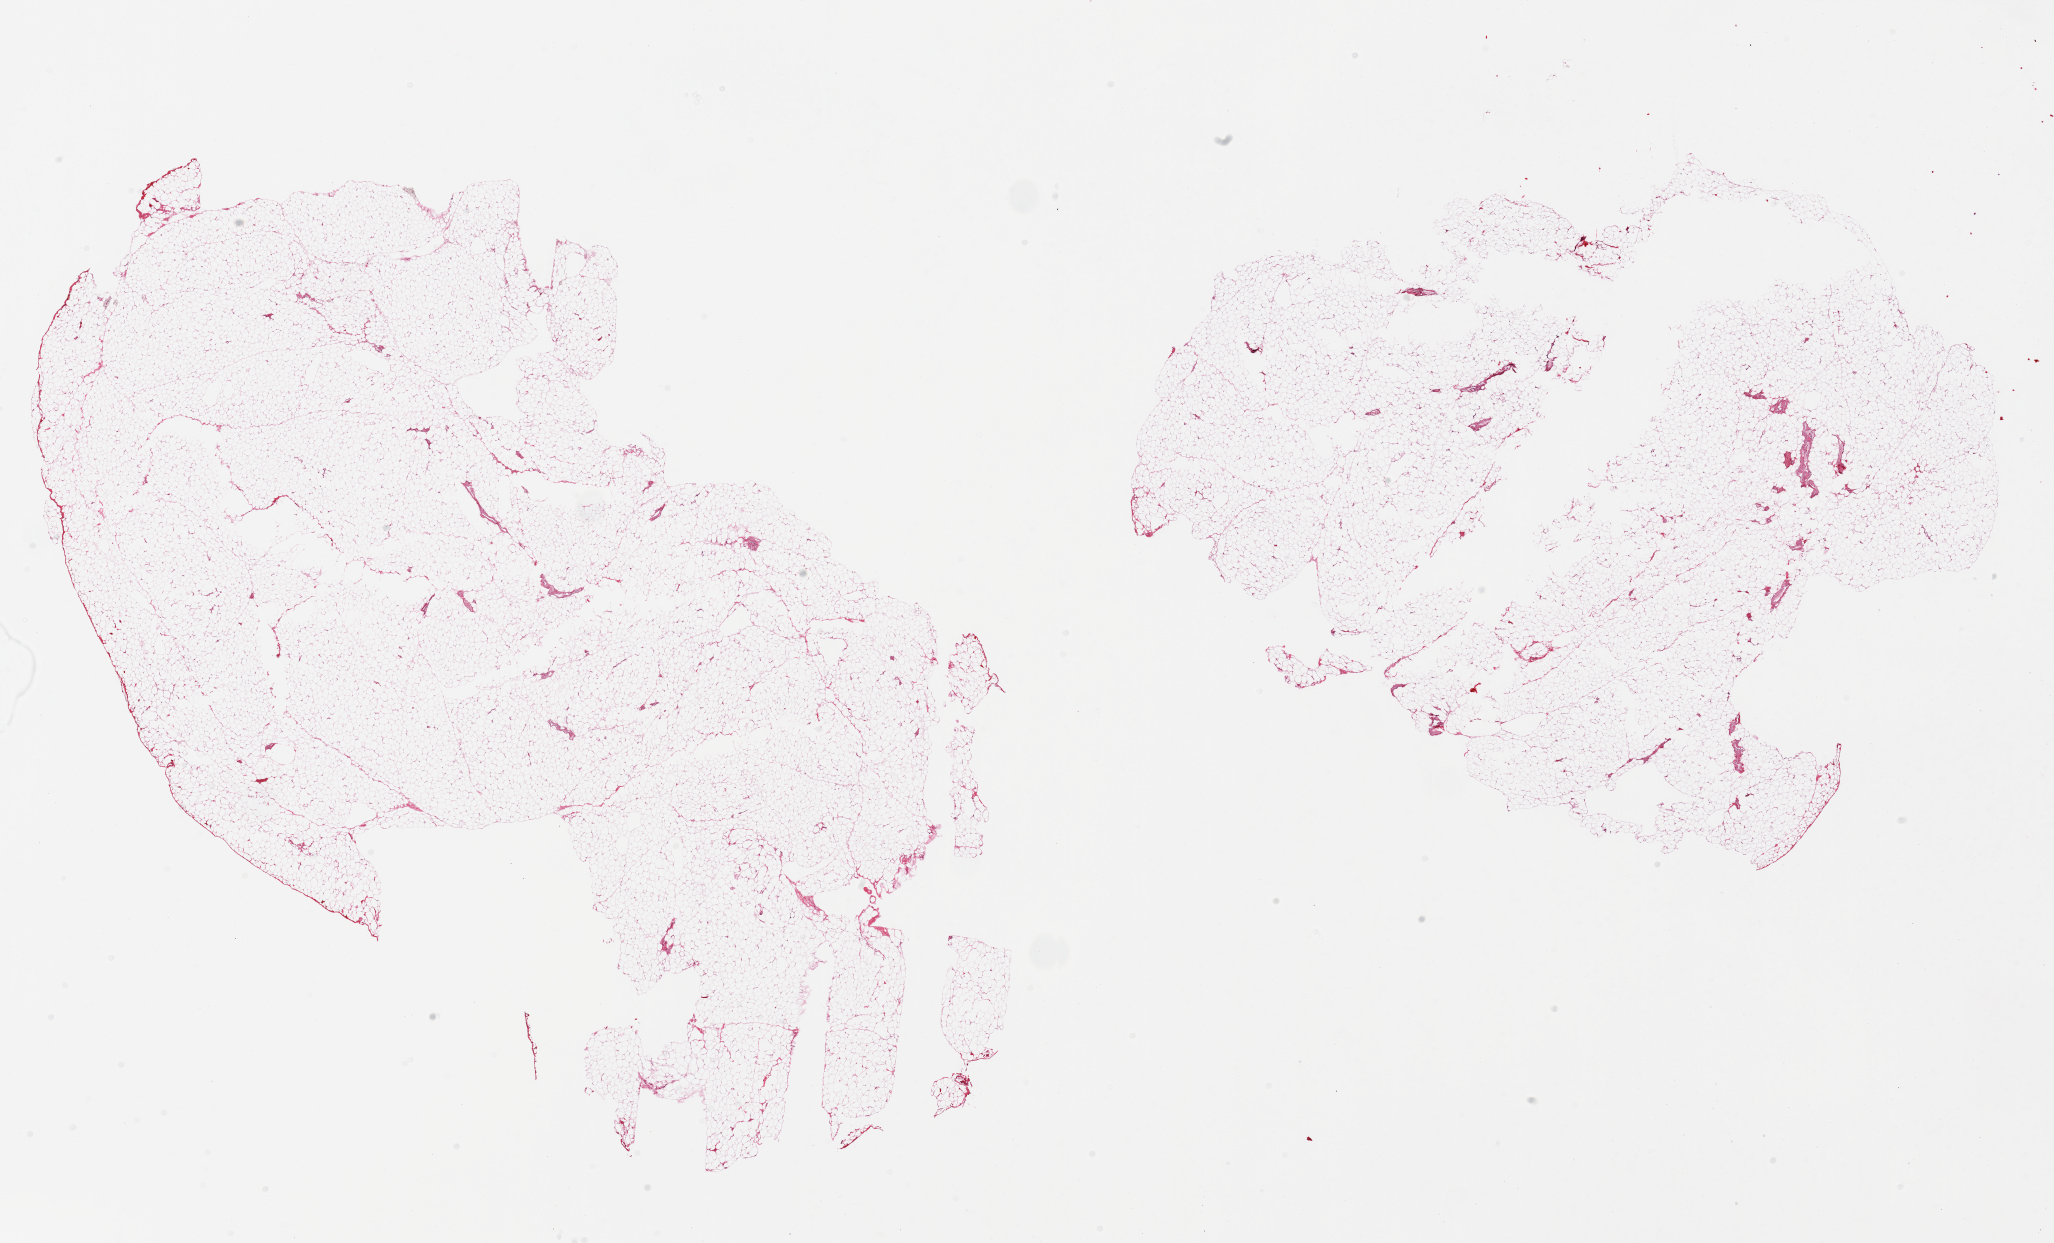
Digitized haematoxylin and eosin-stained section, low-resolution overview of the scanned area, about 32.5 x 19.7 mm (slide scanned at 20x); PAXgene-fixed paraffin-embedded (PFPE) section; section of omentum (target tissue); donor tissue sample.
Reviewer comment on this tissue sample: 2 pieces, minimal fibrosis.